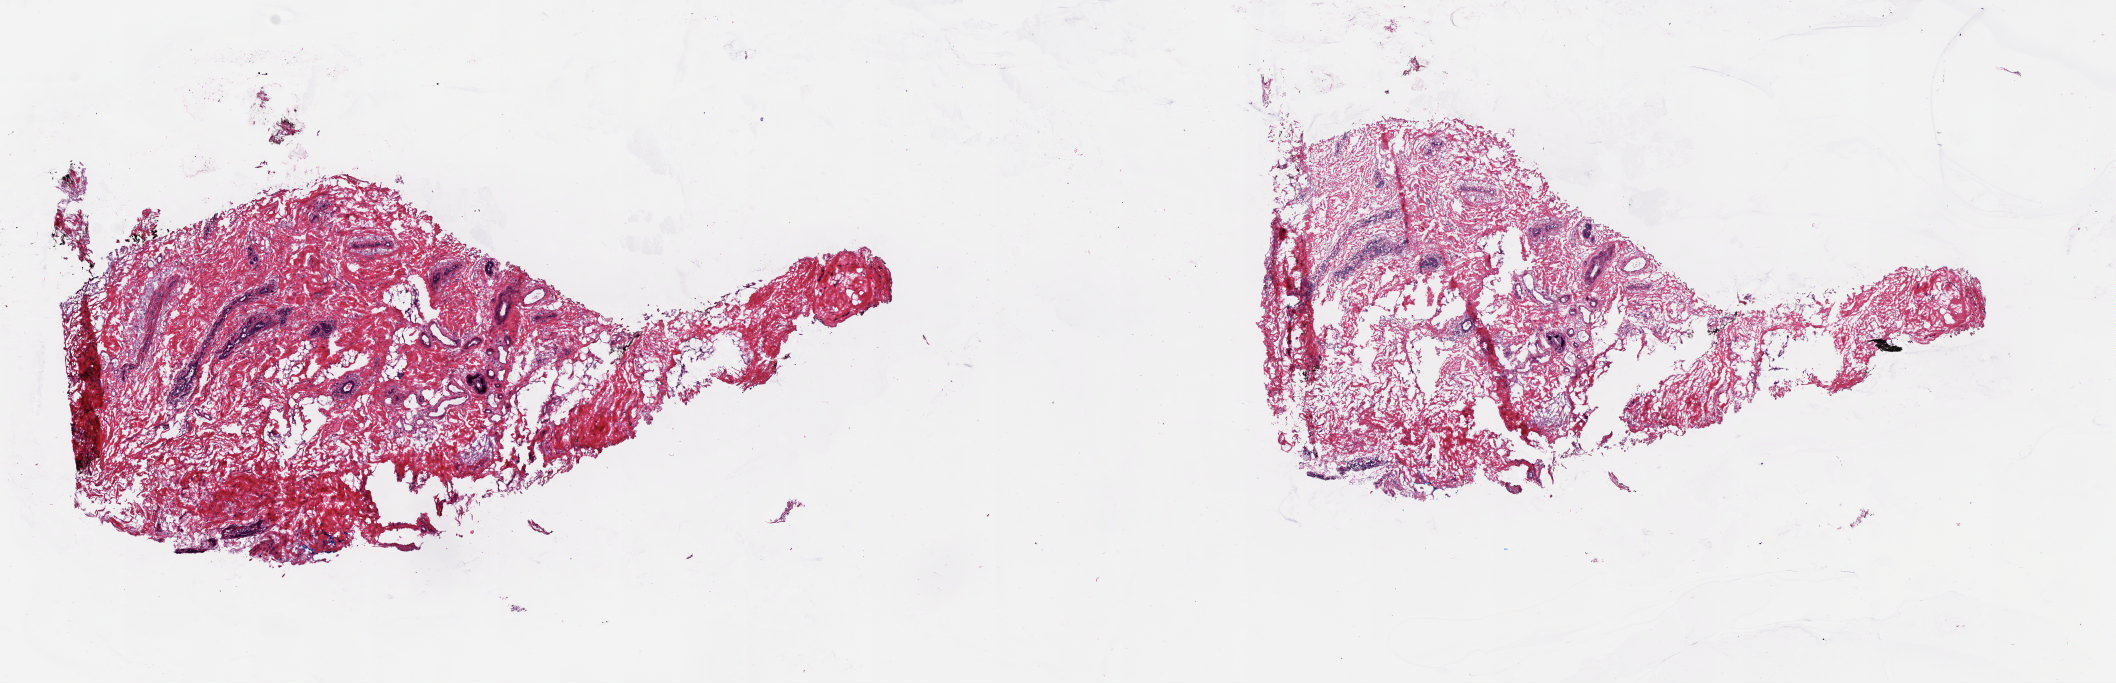
Digitized Hematoxylin and eosin (H&E) stained tissue section (whole slide) — low-resolution overview of the scanned area, about 16.8 x 5.4 mm; frozen section; solid tissue normal (non-tumour tissue) sample from the breast. Patient sex: female. Slide review estimates, as recorded: tumour cells 0%, tumour nuclei 0%, normal cells 22%, stromal cells 78%, necrosis 0%. Infiltration values recorded for this section: lymphocyte infiltration 2%, monocyte infiltration 0%, neutrophil infiltration 0%.
• this section: solid tissue normal (non-tumour) sample from the same patient
• patient diagnosis: Infiltrating duct carcinoma, NOS